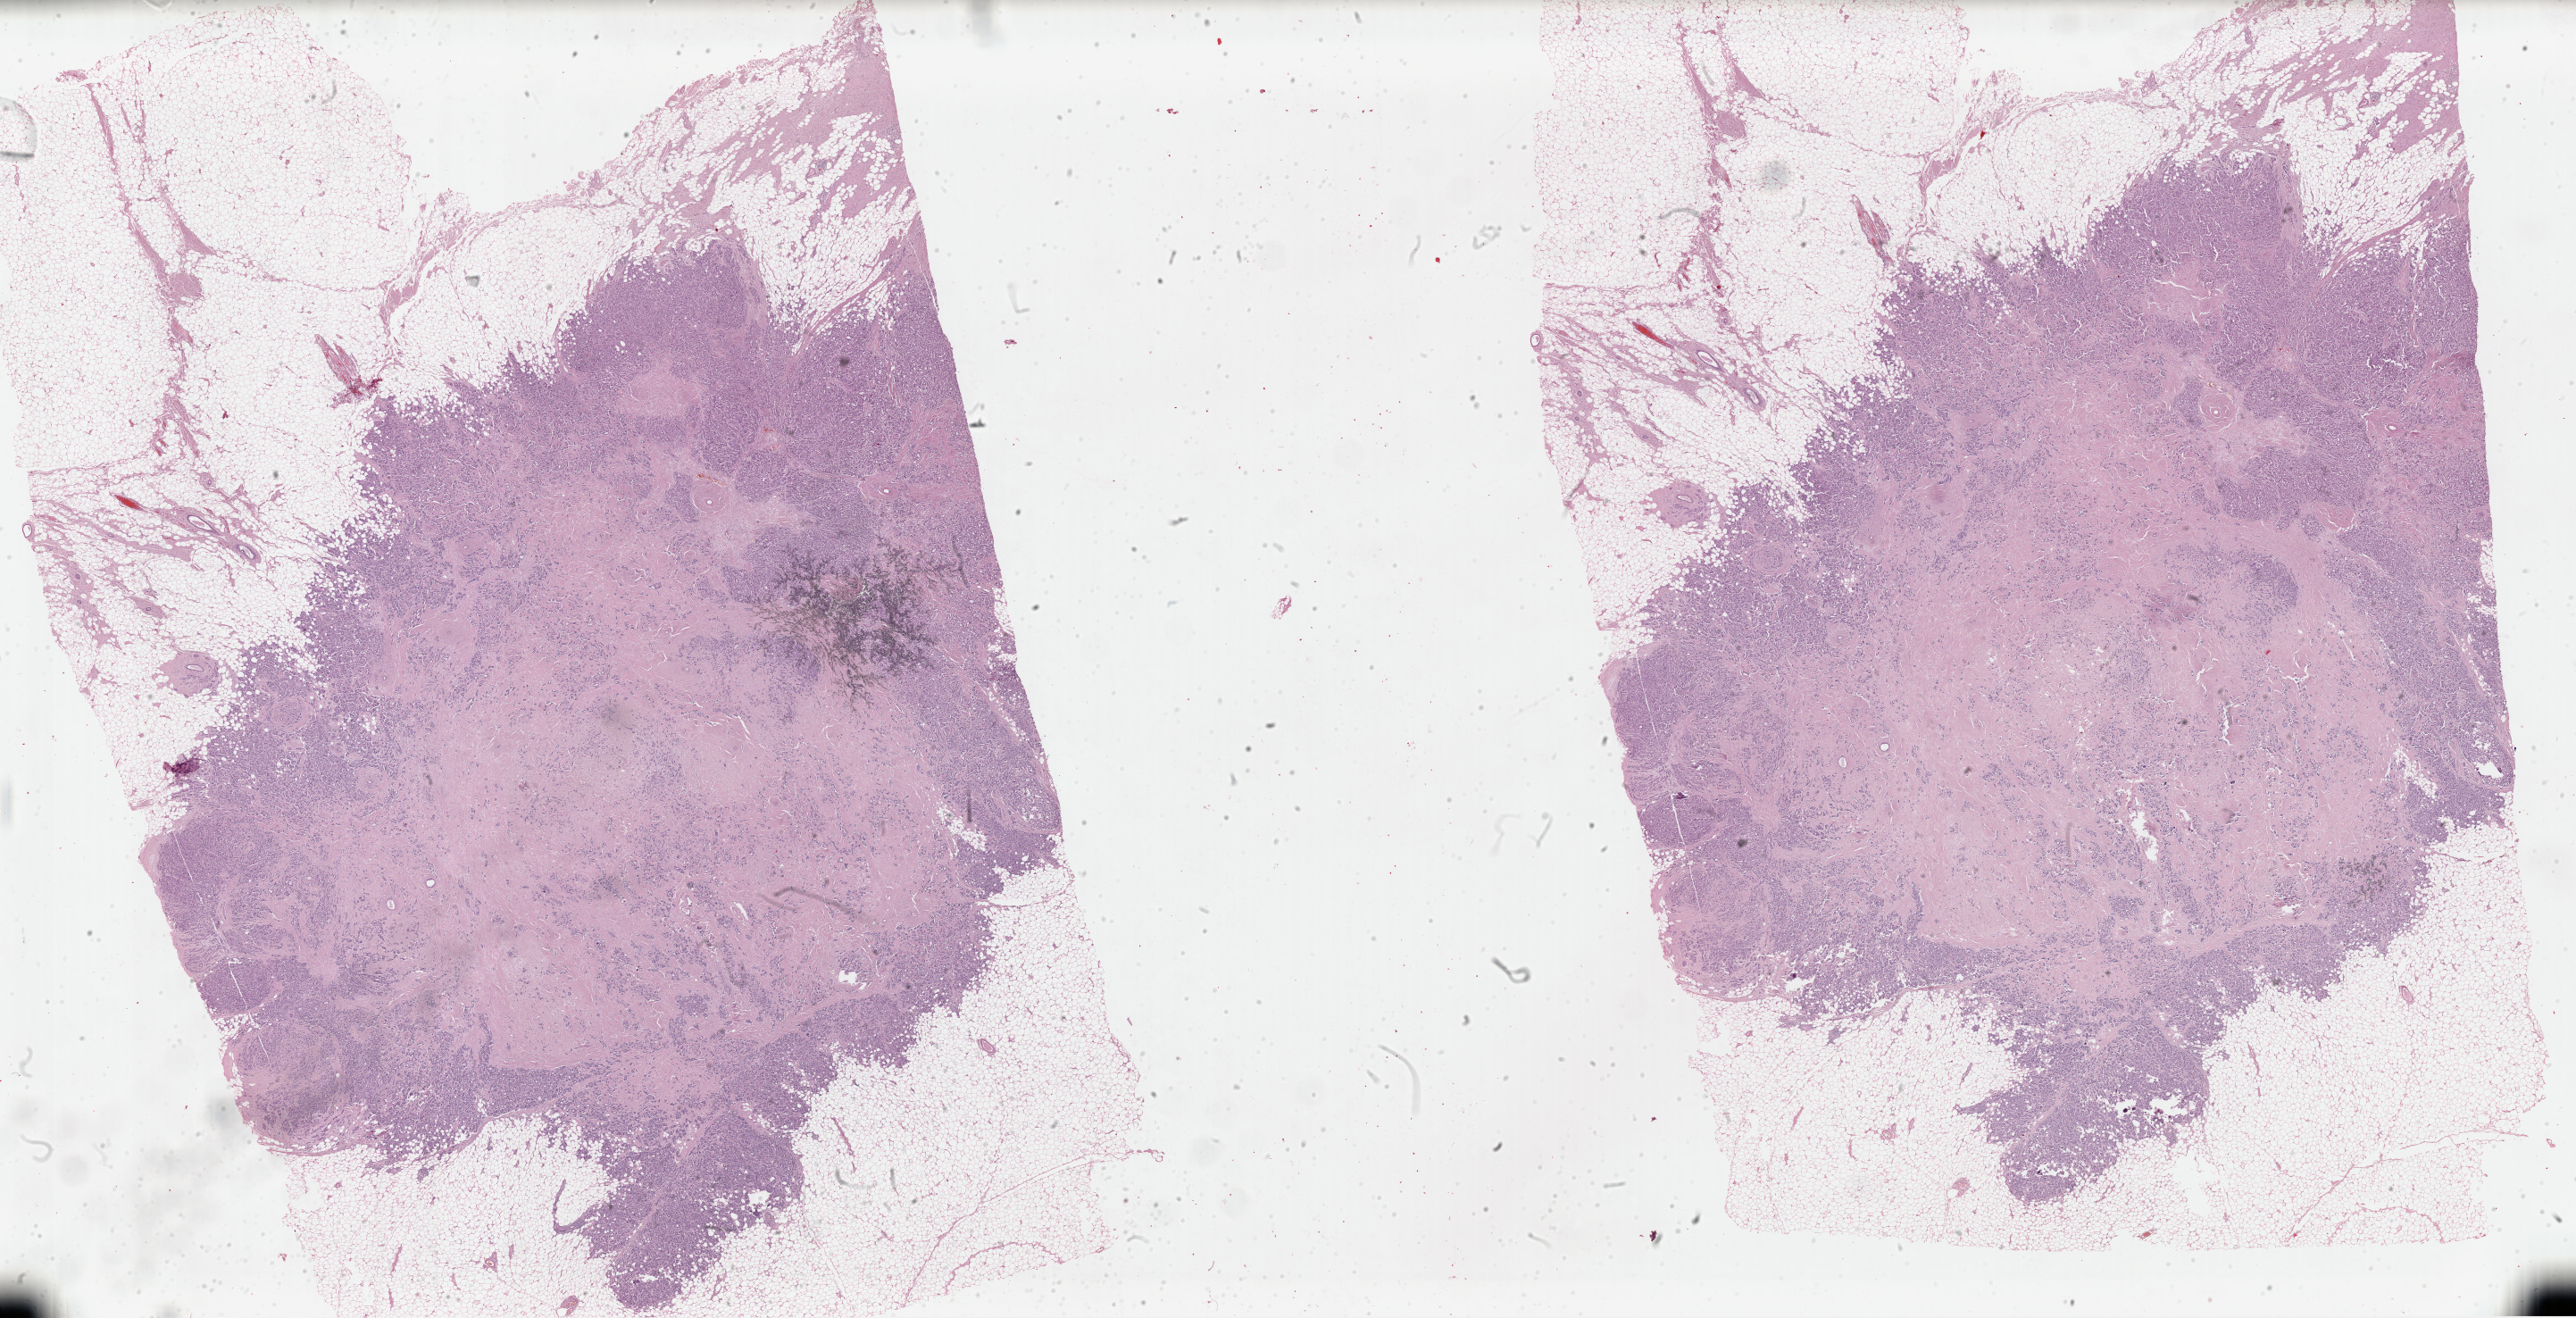
Digitized H&E tissue section (whole slide) — low-resolution overview of the scanned area, about 45.6 x 23.3 mm, FFPE section, sample: primary tumour, breast. Female, age 56 years at initial diagnosis.
Laterality: right. Lymph nodes positive (case pathology): 2 of 7 examined. Diagnosis: Infiltrating duct carcinoma, NOS. AJCC pathologic stage: IIB (7th edition).